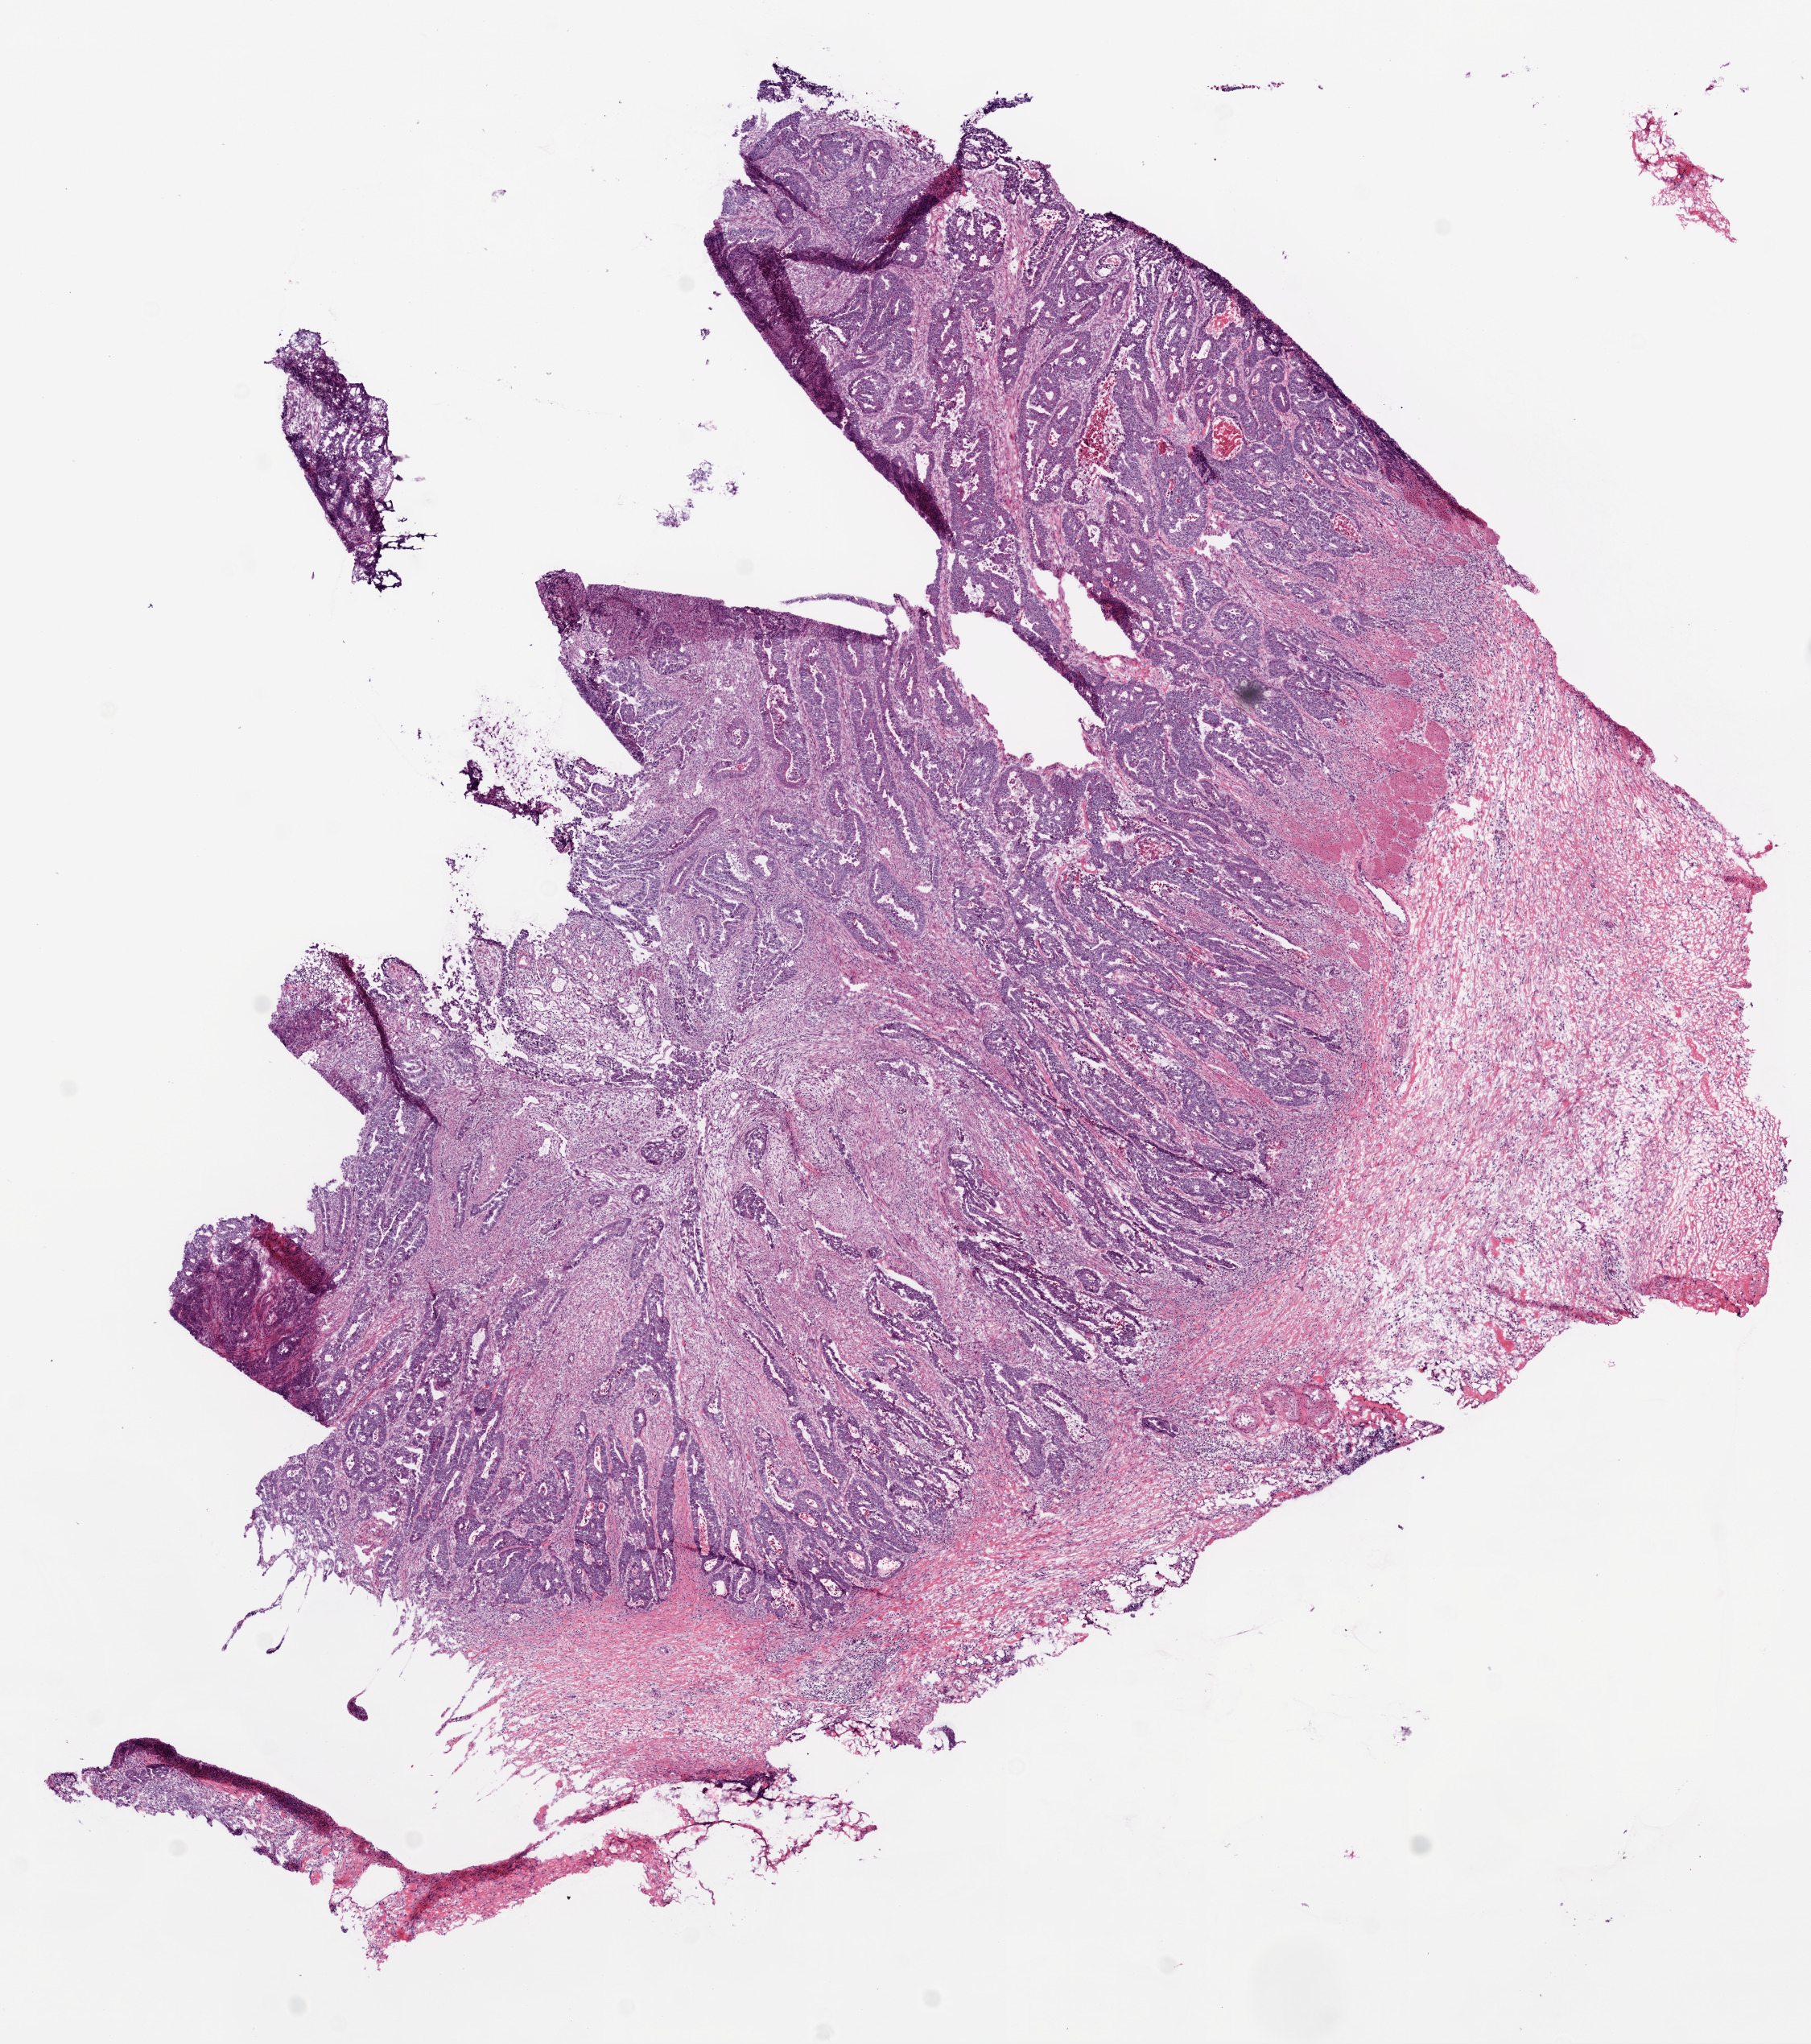
Whole-slide histology image, H&E, whole scanned area (about 9.0 x 10.2 mm) shown as a low-resolution overview. Frozen section. Rectum, primary tumour sample. Female patient; age at initial diagnosis 74 years. Composition of this section per pathologist review: tumour cells 55%, tumour nuclei 75%, normal cells 0%, stromal cells 40%, necrosis 5%.
• TNM: T3 N0 M0
• AJCC pathologic stage: IIA
• lymph nodes positive (case pathology): 0 of 29 examined
• pathologic diagnosis: Adenocarcinoma, NOS (rectosigmoid junction)